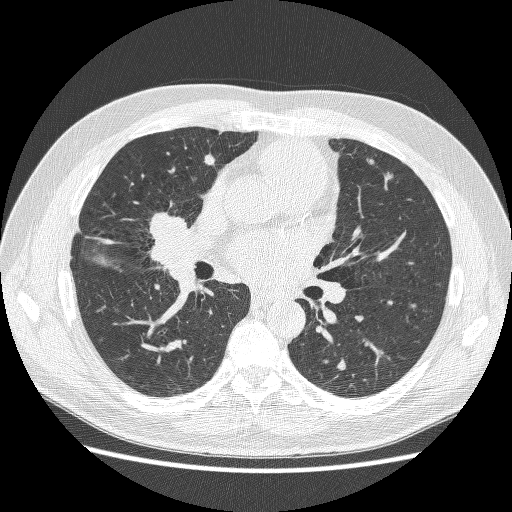
Low-dose screening chest CT, axial slice. Baseline annual screen. Lung window (W 1500 / L -600 HU). Lung (sharp) reconstruction kernel (BONE). Slice 146 of 251 in the series. 512 × 512 image matrix, field of view 360 × 360 mm. Male, age 59 years at enrolment. Former smoker at enrolment.
- Expert reader's lesion annotation, bounding box [x1, y1, x2, y2] px = [127, 204, 198, 270].
- No non-calcified nodule or mass ≥4 mm was recorded by the screening reader at this exam.
- Official screen result: positive, change unspecified: nodule(s) >= 4 mm or enlarging nodule(s), mass(es), or other non-specific abnormalities suspicious for lung cancer.
- Participant outcome: lung cancer diagnosed 24 days after this screen — adenocarcinoma, NOS, right middle lobe, poorly differentiated (G3), stage IV (AJCC 6th edition), 54 mm at pathology.